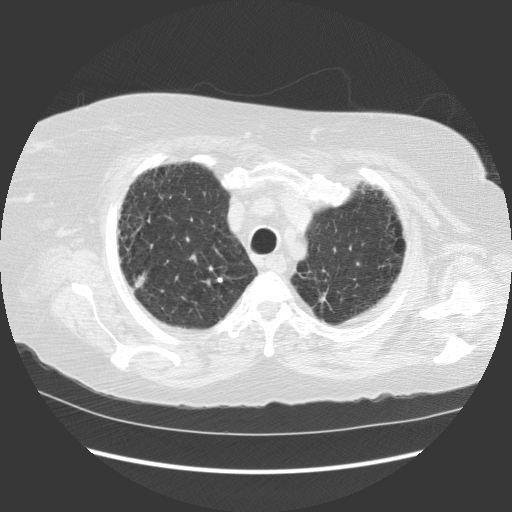
Axial slice from a low-dose chest CT screening exam, first (baseline) screen, lung window (W 1500 / L -600 HU), 2.5 mm slice thickness, standard (soft-tissue) reconstruction kernel (STANDARD), 140 kVp, slice 100 of 121 in the series. Female, age 64 years at enrolment.
• Lesion marked by an expert reader, bounding box <112,257,165,301> (left, top, right, bottom; pixels).
• The screening reader recorded 2 non-calcified nodules or masses ≥4 mm on this exam (right upper lobe, left upper lobe); which of them this box marks is not recorded.